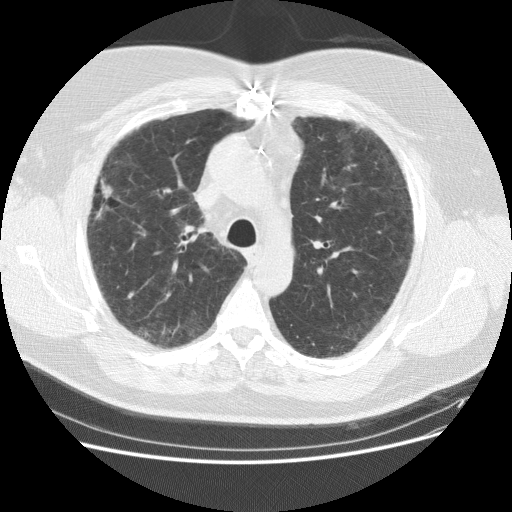
Chest CT (low-dose screening protocol), one axial image, baseline screening round, lung window (W 1500 / L -600 HU), 2.5 mm slice thickness, standard (soft-tissue) reconstruction kernel (STANDARD), 512 × 512 image matrix, field of view 378 × 378 mm. Male, age 59 years at enrolment.
Lesion marked by an expert reader, bounding box <78,159,131,245> (left, top, right, bottom; pixels). The screening reader recorded 2 non-calcified nodules or masses ≥4 mm on this exam (right middle lobe, right lower lobe); which of them this box marks is not recorded. Official screen result: positive, change unspecified: nodule(s) >= 4 mm or enlarging nodule(s), mass(es), or other non-specific abnormalities suspicious for lung cancer. Participant outcome: lung cancer diagnosed 338 days after this screen — adenocarcinoma, NOS, right upper lobe, right middle lobe, moderately differentiated (G2), stage IA (AJCC 6th edition), 13 mm at pathology.